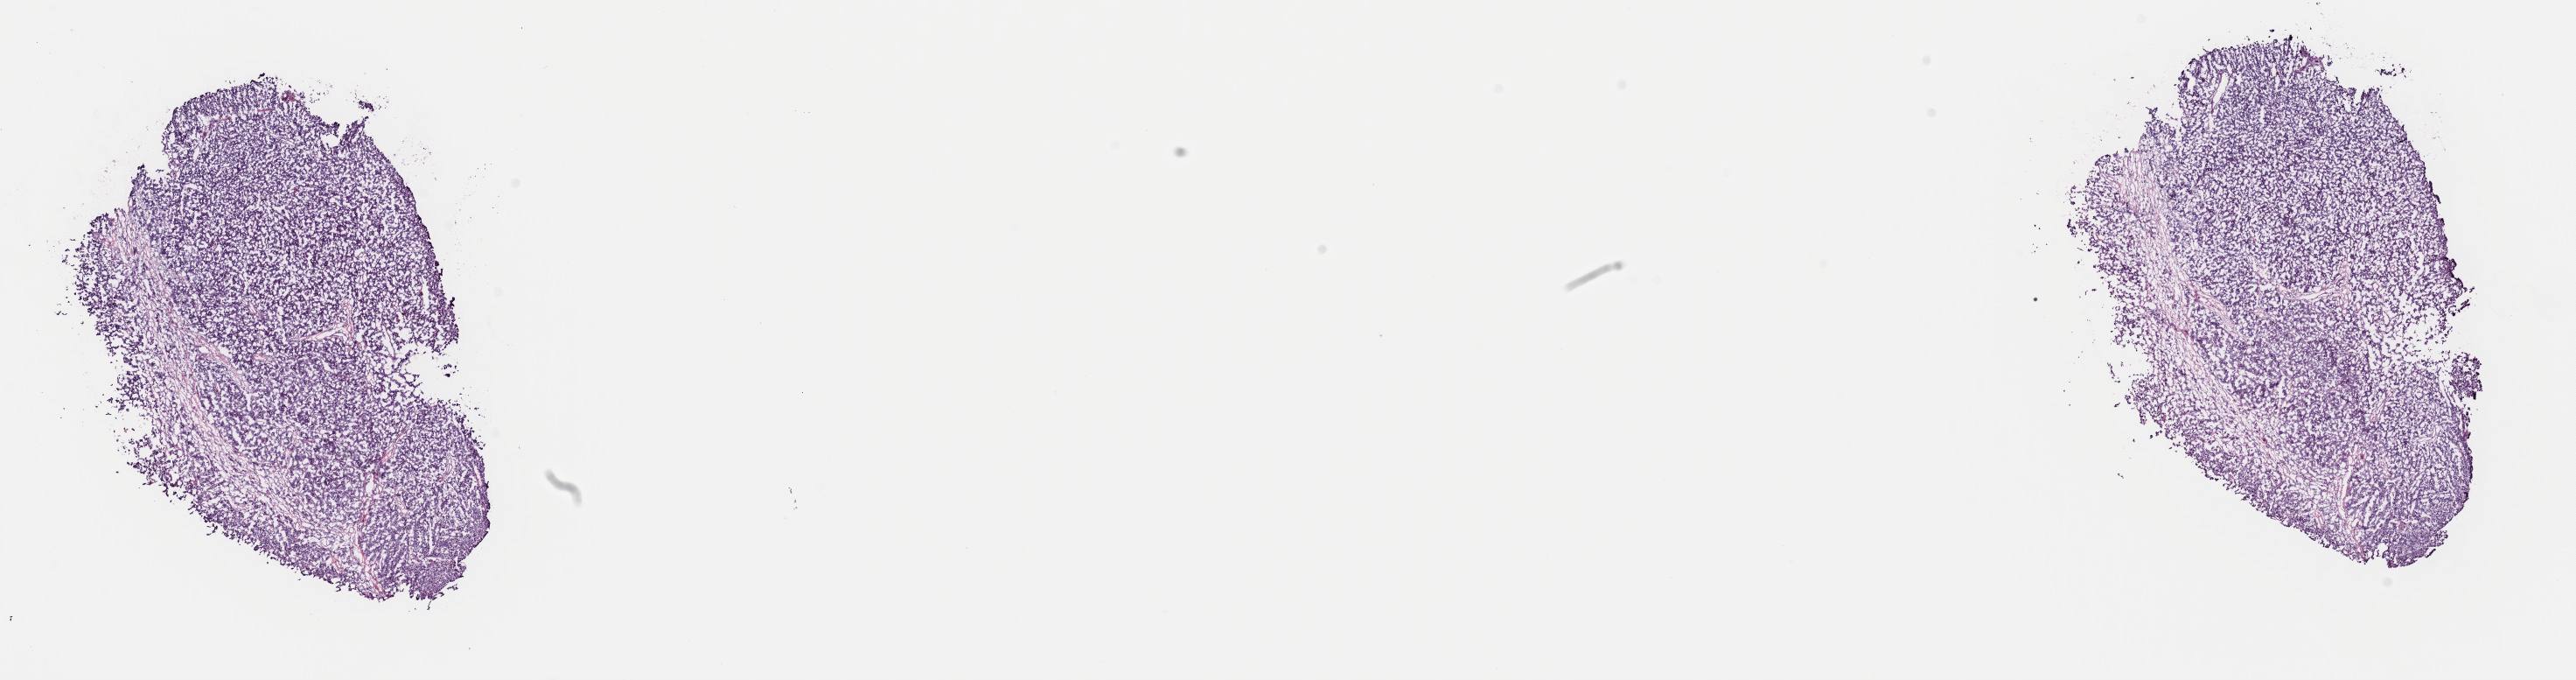
Digitized H&E-stained tissue section (whole slide) — a low-resolution overview of the entire scanned area, about 23.3 x 6.1 mm (from a 40x scan), frozen section from the top of the tissue portion, primary tumour sample from the liver. Patient: male, age at initial diagnosis 64 years. Histologic grade: G1 (well differentiated). Slide review estimates, as recorded: tumour cells 100%, tumour nuclei 80%, normal cells 0%, stromal cells 0%, necrosis 0%. Infiltration values recorded for this section: lymphocyte infiltration 1%, monocyte infiltration 0%, neutrophil infiltration 0%.
AJCC pathologic stage: I (7th edition). Histologic diagnosis: Combined hepatocellular carcinoma and cholangiocarcinoma.